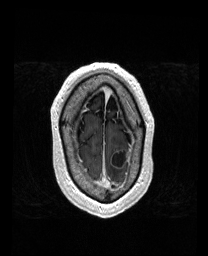
Brain MRI from a brain-tumour surgery series, one axial slice. Slice 154 of 192 in the series (ordered by position). T1-weighted post-contrast. 208 × 256 image matrix, field of view 211 × 260 mm. From the clinical record (not read from this slice): histopathology: Metastatic Carcinoma from Lung Adenocarcinoma.
Structures marked on this image (outlined manually by an expert reader):
- tumour: bounding box (x1, y1, x2, y2) in pixels: (112, 149, 128, 167)